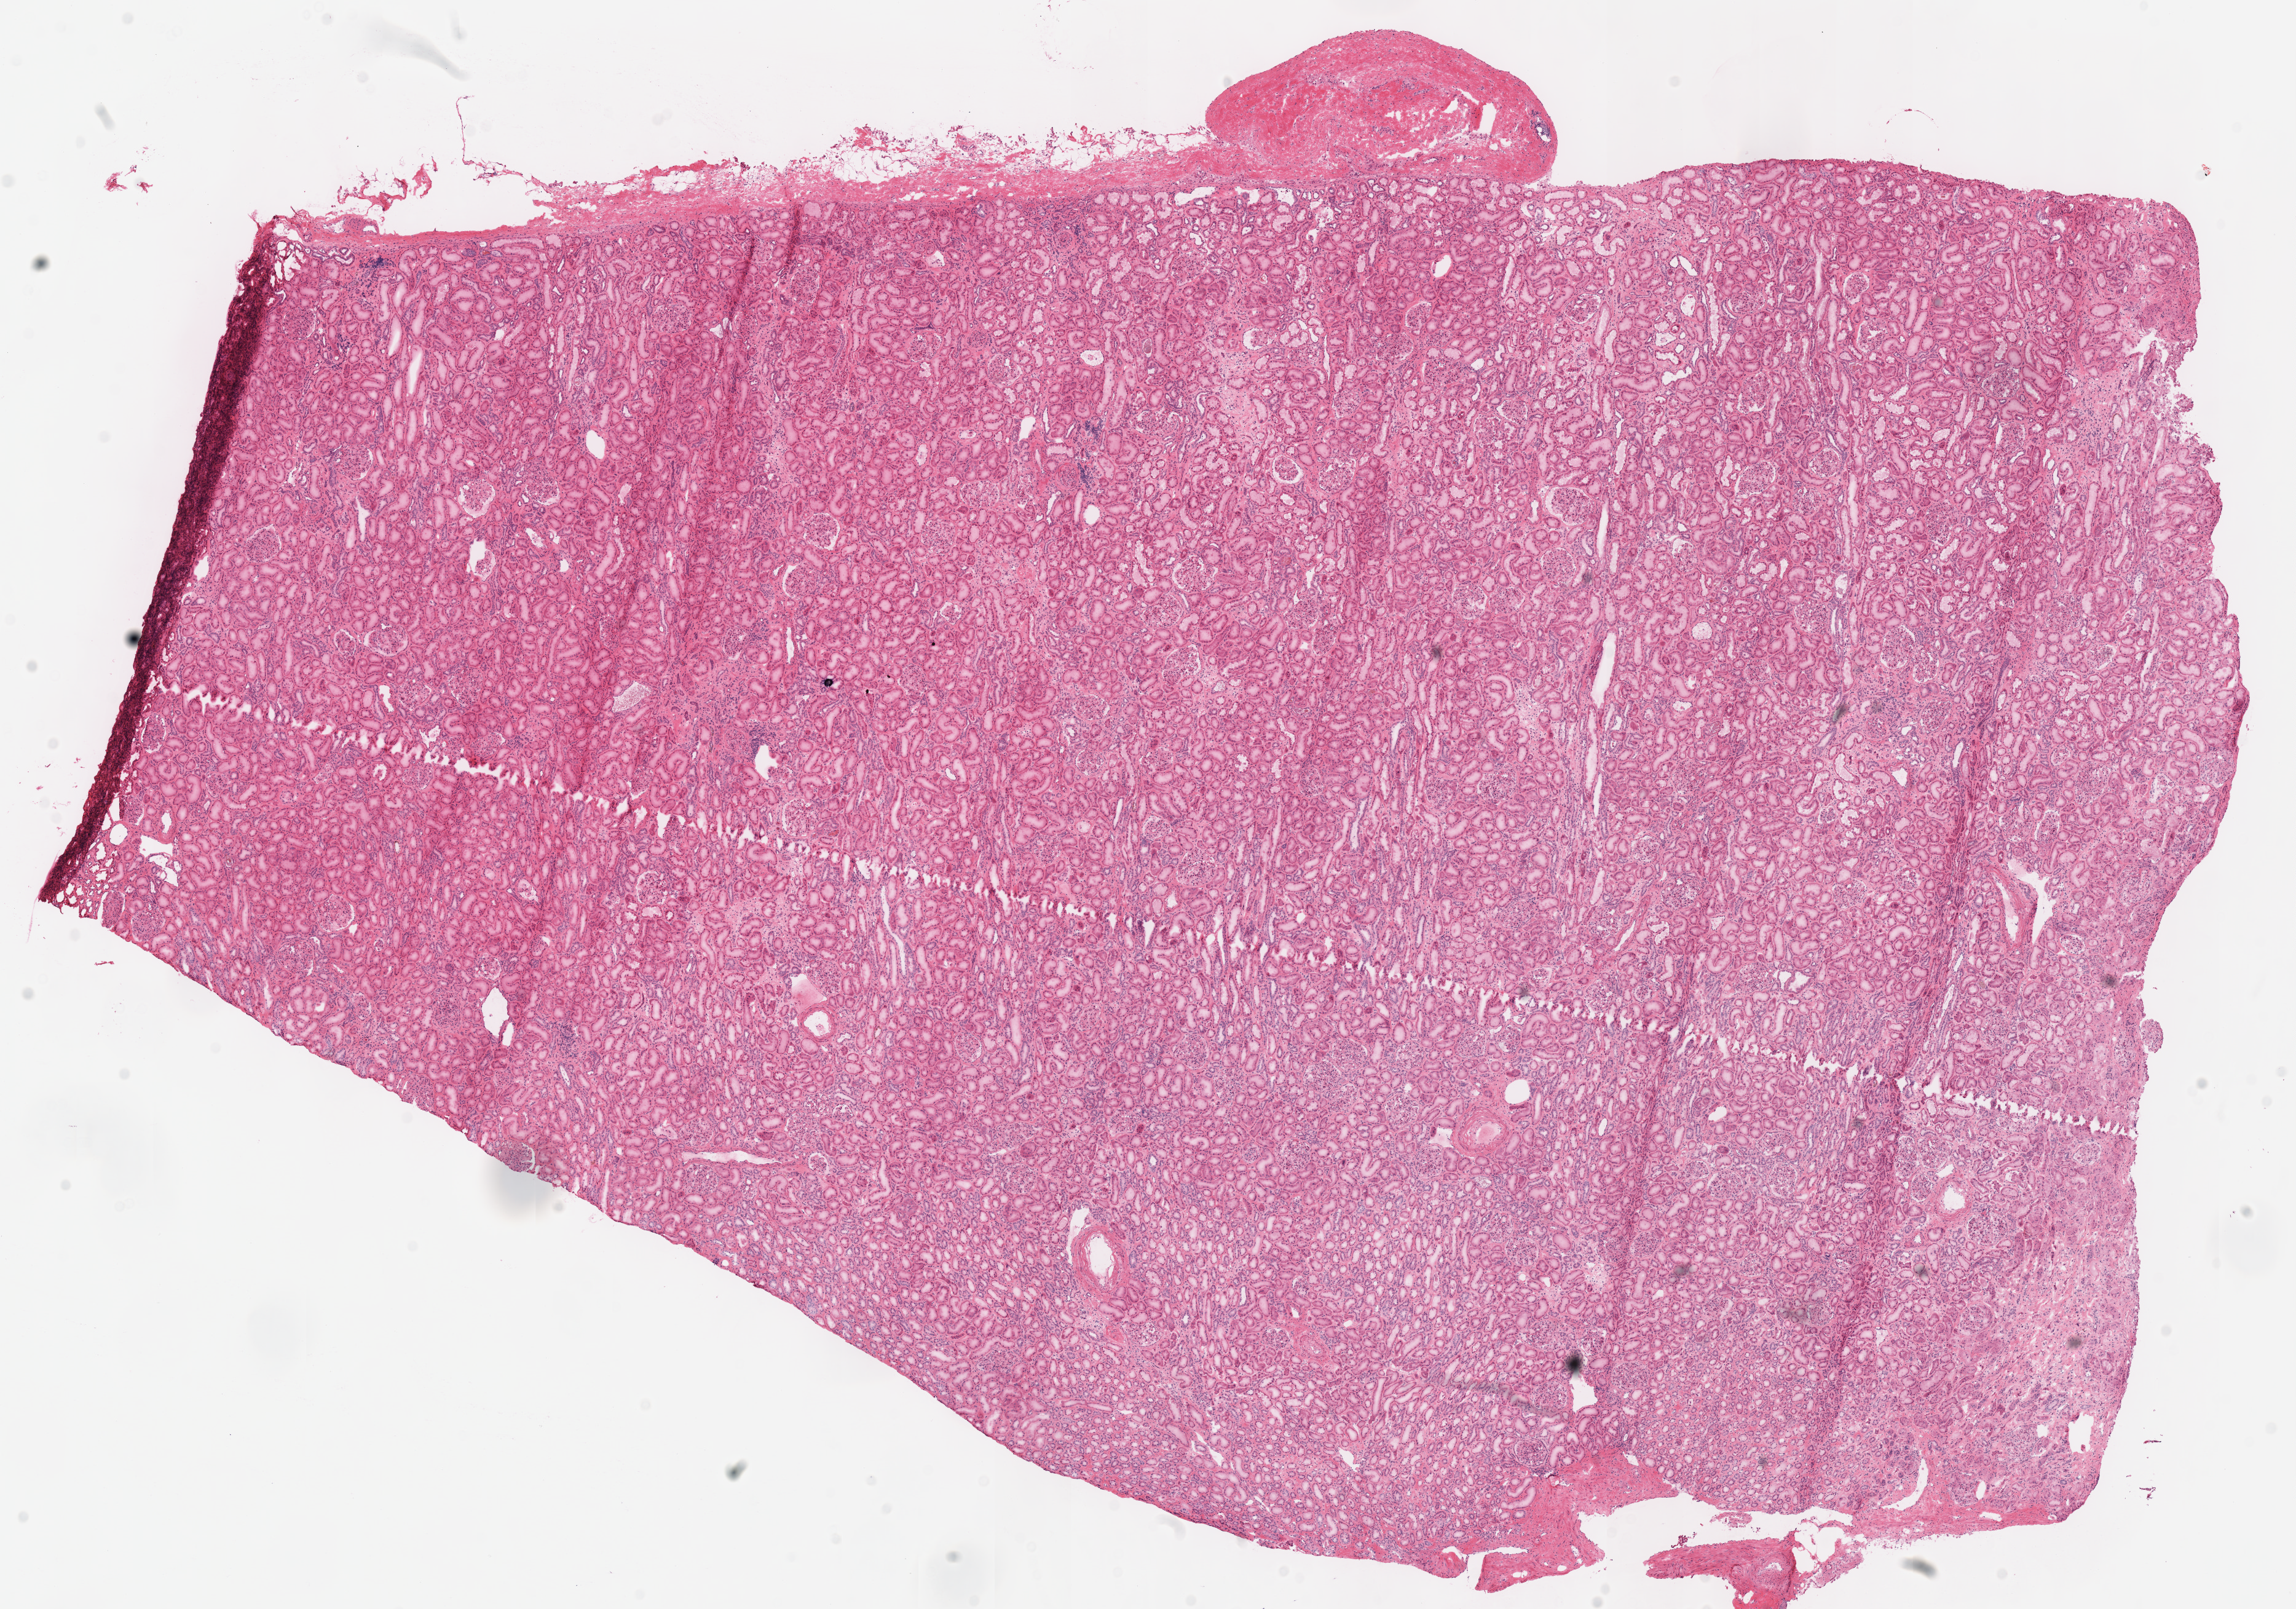
Digitized H&E tissue section (whole slide) — a low-resolution overview of the entire scanned area, about 14.7 x 10.3 mm (slide scanned at 40x), frozen section from the top of the tissue portion, sample: solid tissue normal (non-tumour tissue), kidney. Male patient; age at initial diagnosis 67 years. Infiltration values recorded for this section: lymphocyte infiltration 1%, monocyte infiltration 0%, neutrophil infiltration 0%.
This section: solid tissue normal sample (biorepository sample class). Patient diagnosis: Renal cell carcinoma, chromophobe type.